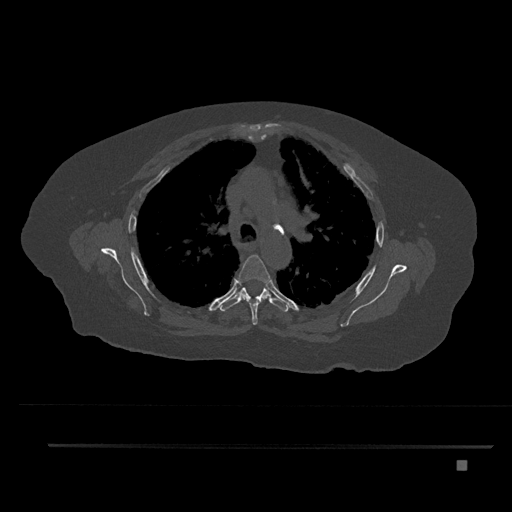
CT including the spine, one axial slice; position 586 of 797 along the scan axis; reconstruction kernel Br40s/3; 120 kVp; bone window (W 1800 / L 400 HU); 512 × 512 image matrix. Patient: female, 76 years. From the clinical record (not read from this slice): primary cancer: lung.
Annotated regions visible in this slice (semi-automatically segmented with operator editing):
- T4 vertebra: box from (x=238, y=255) to (x=271, y=325) px
- T5 vertebra: (x=220, y=282)–(x=289, y=312)